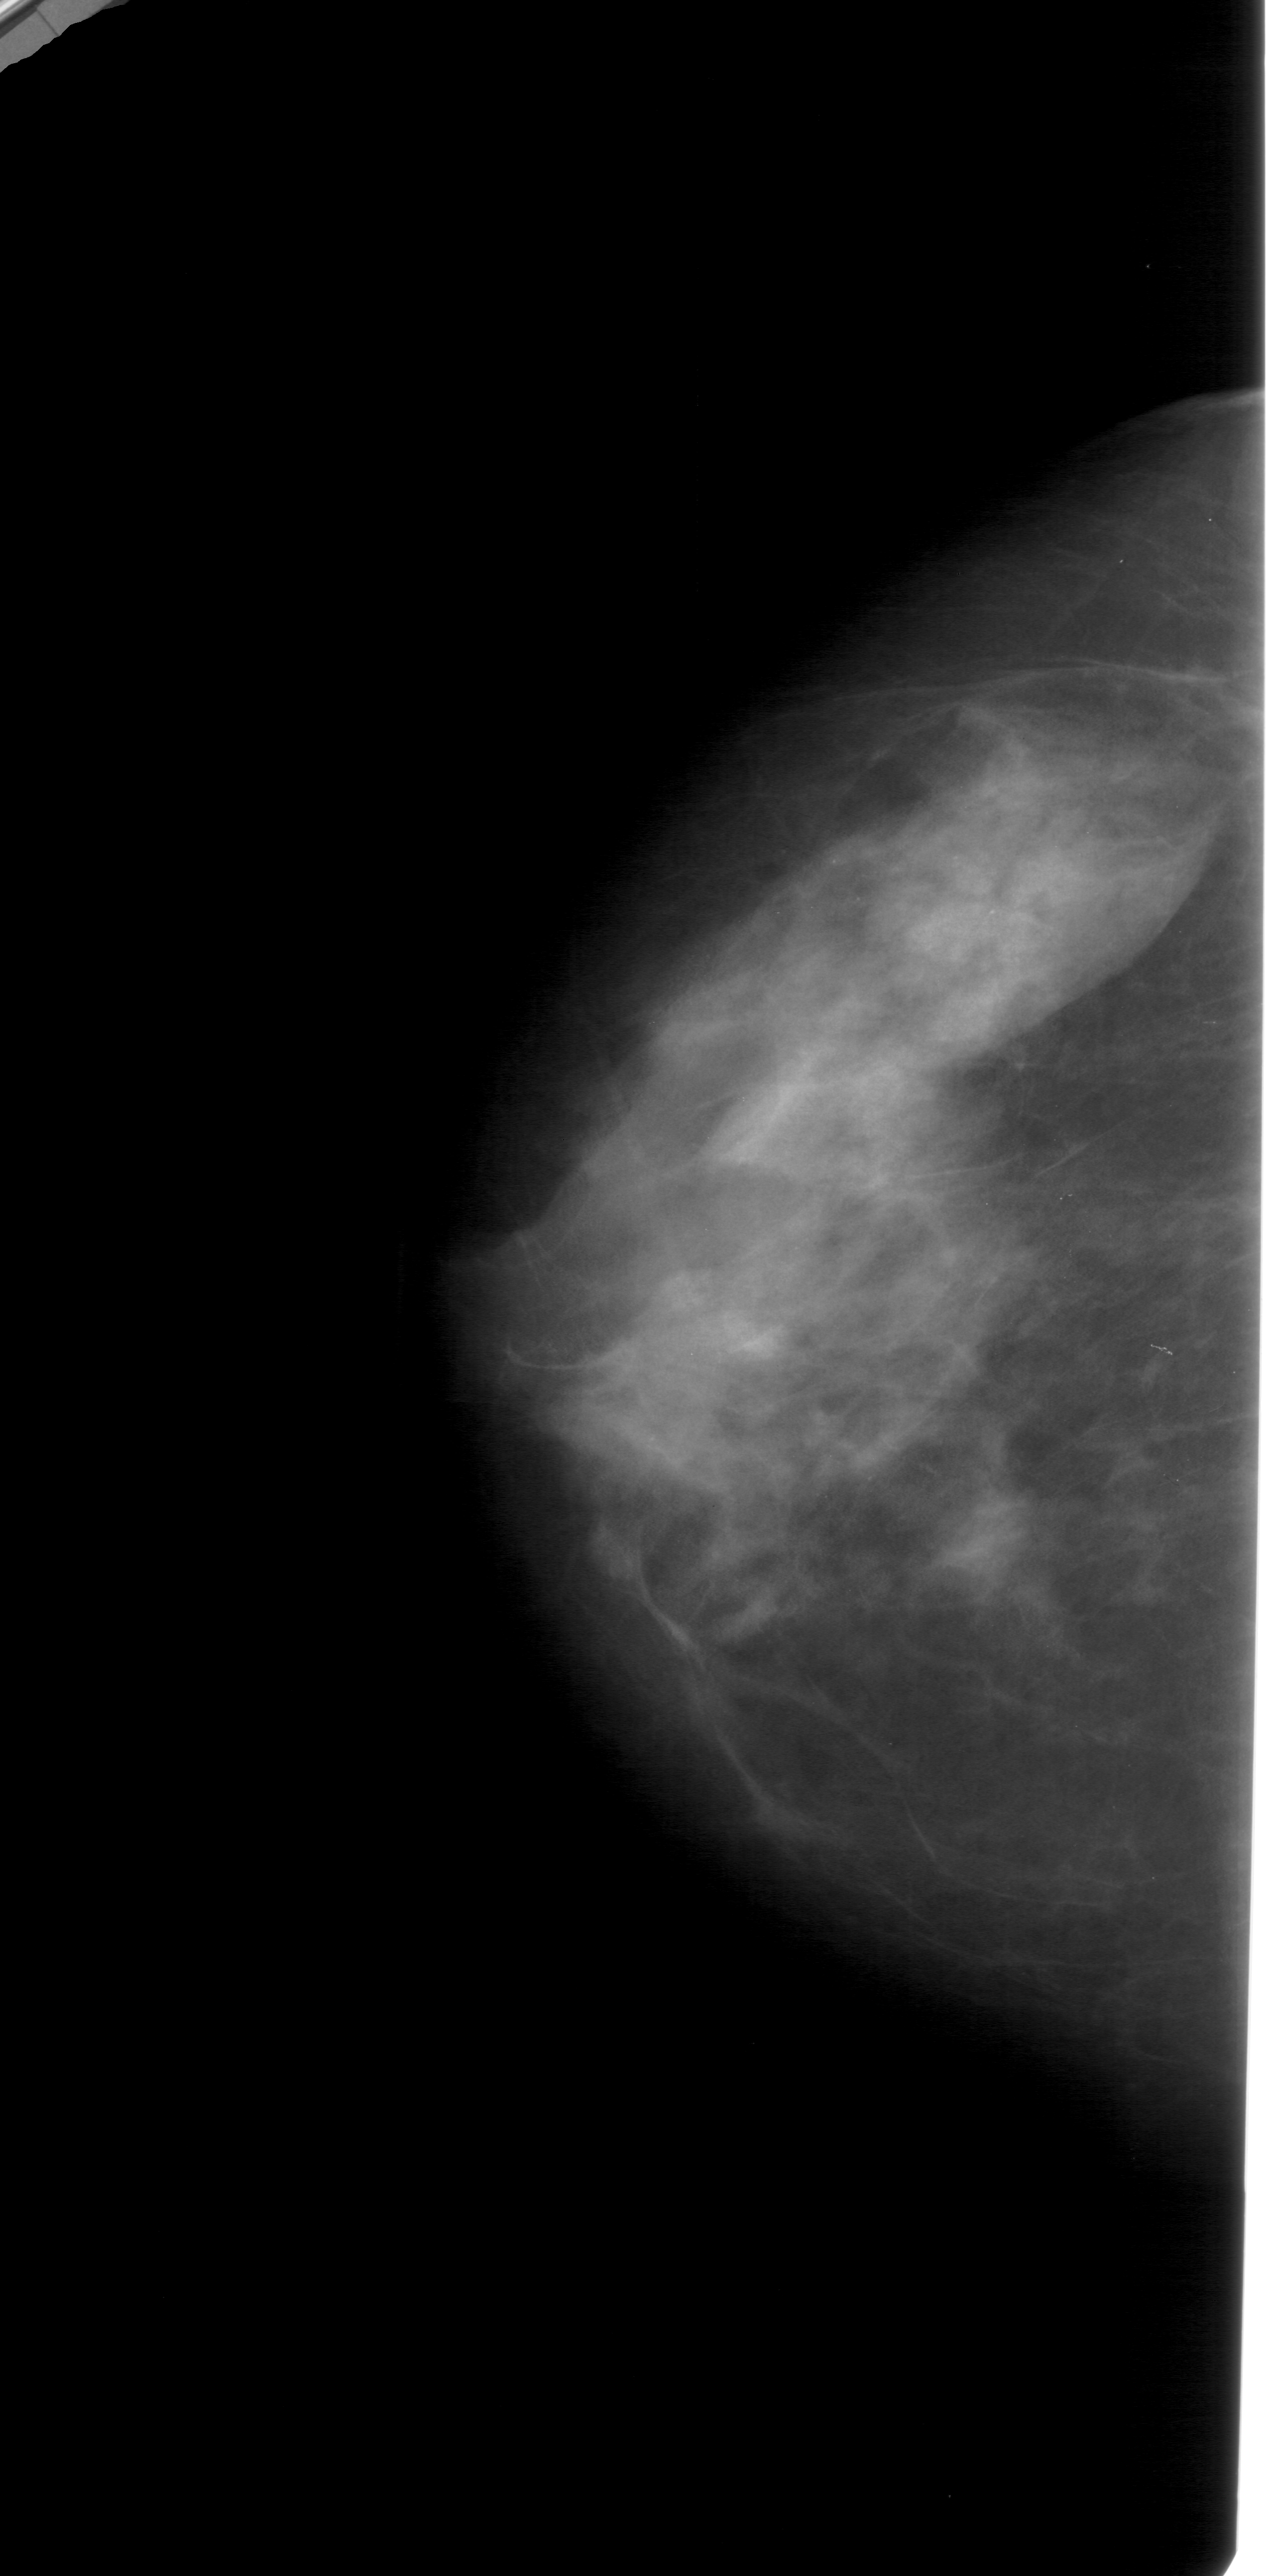
Mammogram (digitized film); left breast; CC view; breast composition: extremely dense (BI-RADS density category 4 of 4).
Radiologist-marked abnormalities on this image: calcifications, morphology punctate, distribution linear; BI-RADS assessment category 4; pathology result (as recorded, not read from the image): benign.